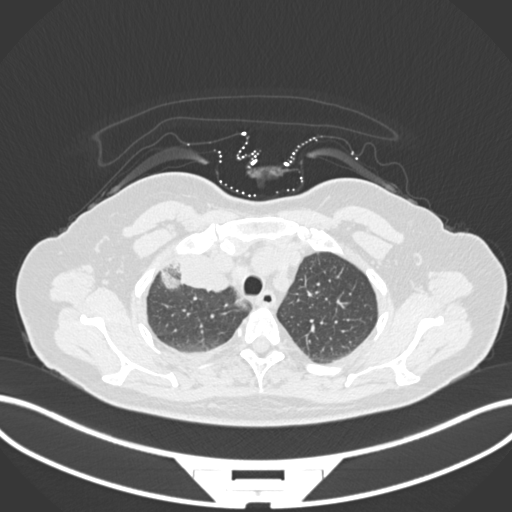
Chest CT, one axial slice; reconstruction kernel B30f; lung window (W 1500 / L -600 HU); 1 mm slice thickness; 512 × 512 image matrix, field of view 400 × 400 mm. Patient: female, 52 years. Case-level facts recorded for this patient, not image findings: clinical TNM (as recorded): T3 N1 M1.
Outlined on this slice (bounding box drawn by a radiologist):
- lung tumour (recorded histology: adenocarcinoma): bounding box (x1, y1, x2, y2) in pixels: (154, 250, 237, 293)